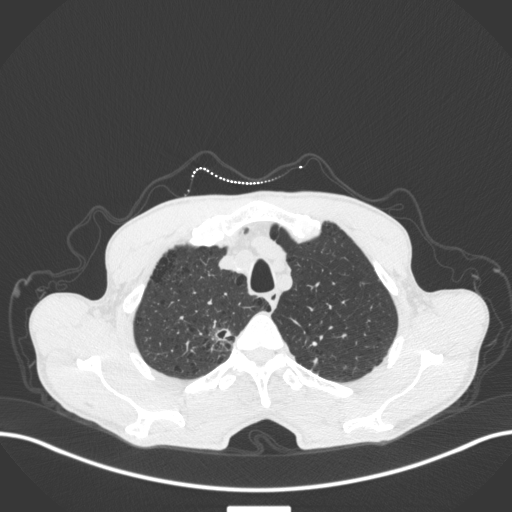
Chest CT, one axial slice. Slice 363 of 445 in the series (ordered by position). Reconstruction kernel B31f. Lung window (W 1500 / L -600 HU). 512 × 512 image matrix, field of view 400 × 400 mm. Patient: male, 70 years. From the clinical record (not read from this slice): clinical TNM (as recorded): T1a N0 M0; histopathological grade: G1-2.
Outlined on this slice (rectangle marked by the reading radiologist):
- lung tumour (recorded histology: adenocarcinoma): bounding box <208,321,232,346> (left, top, right, bottom; pixels)